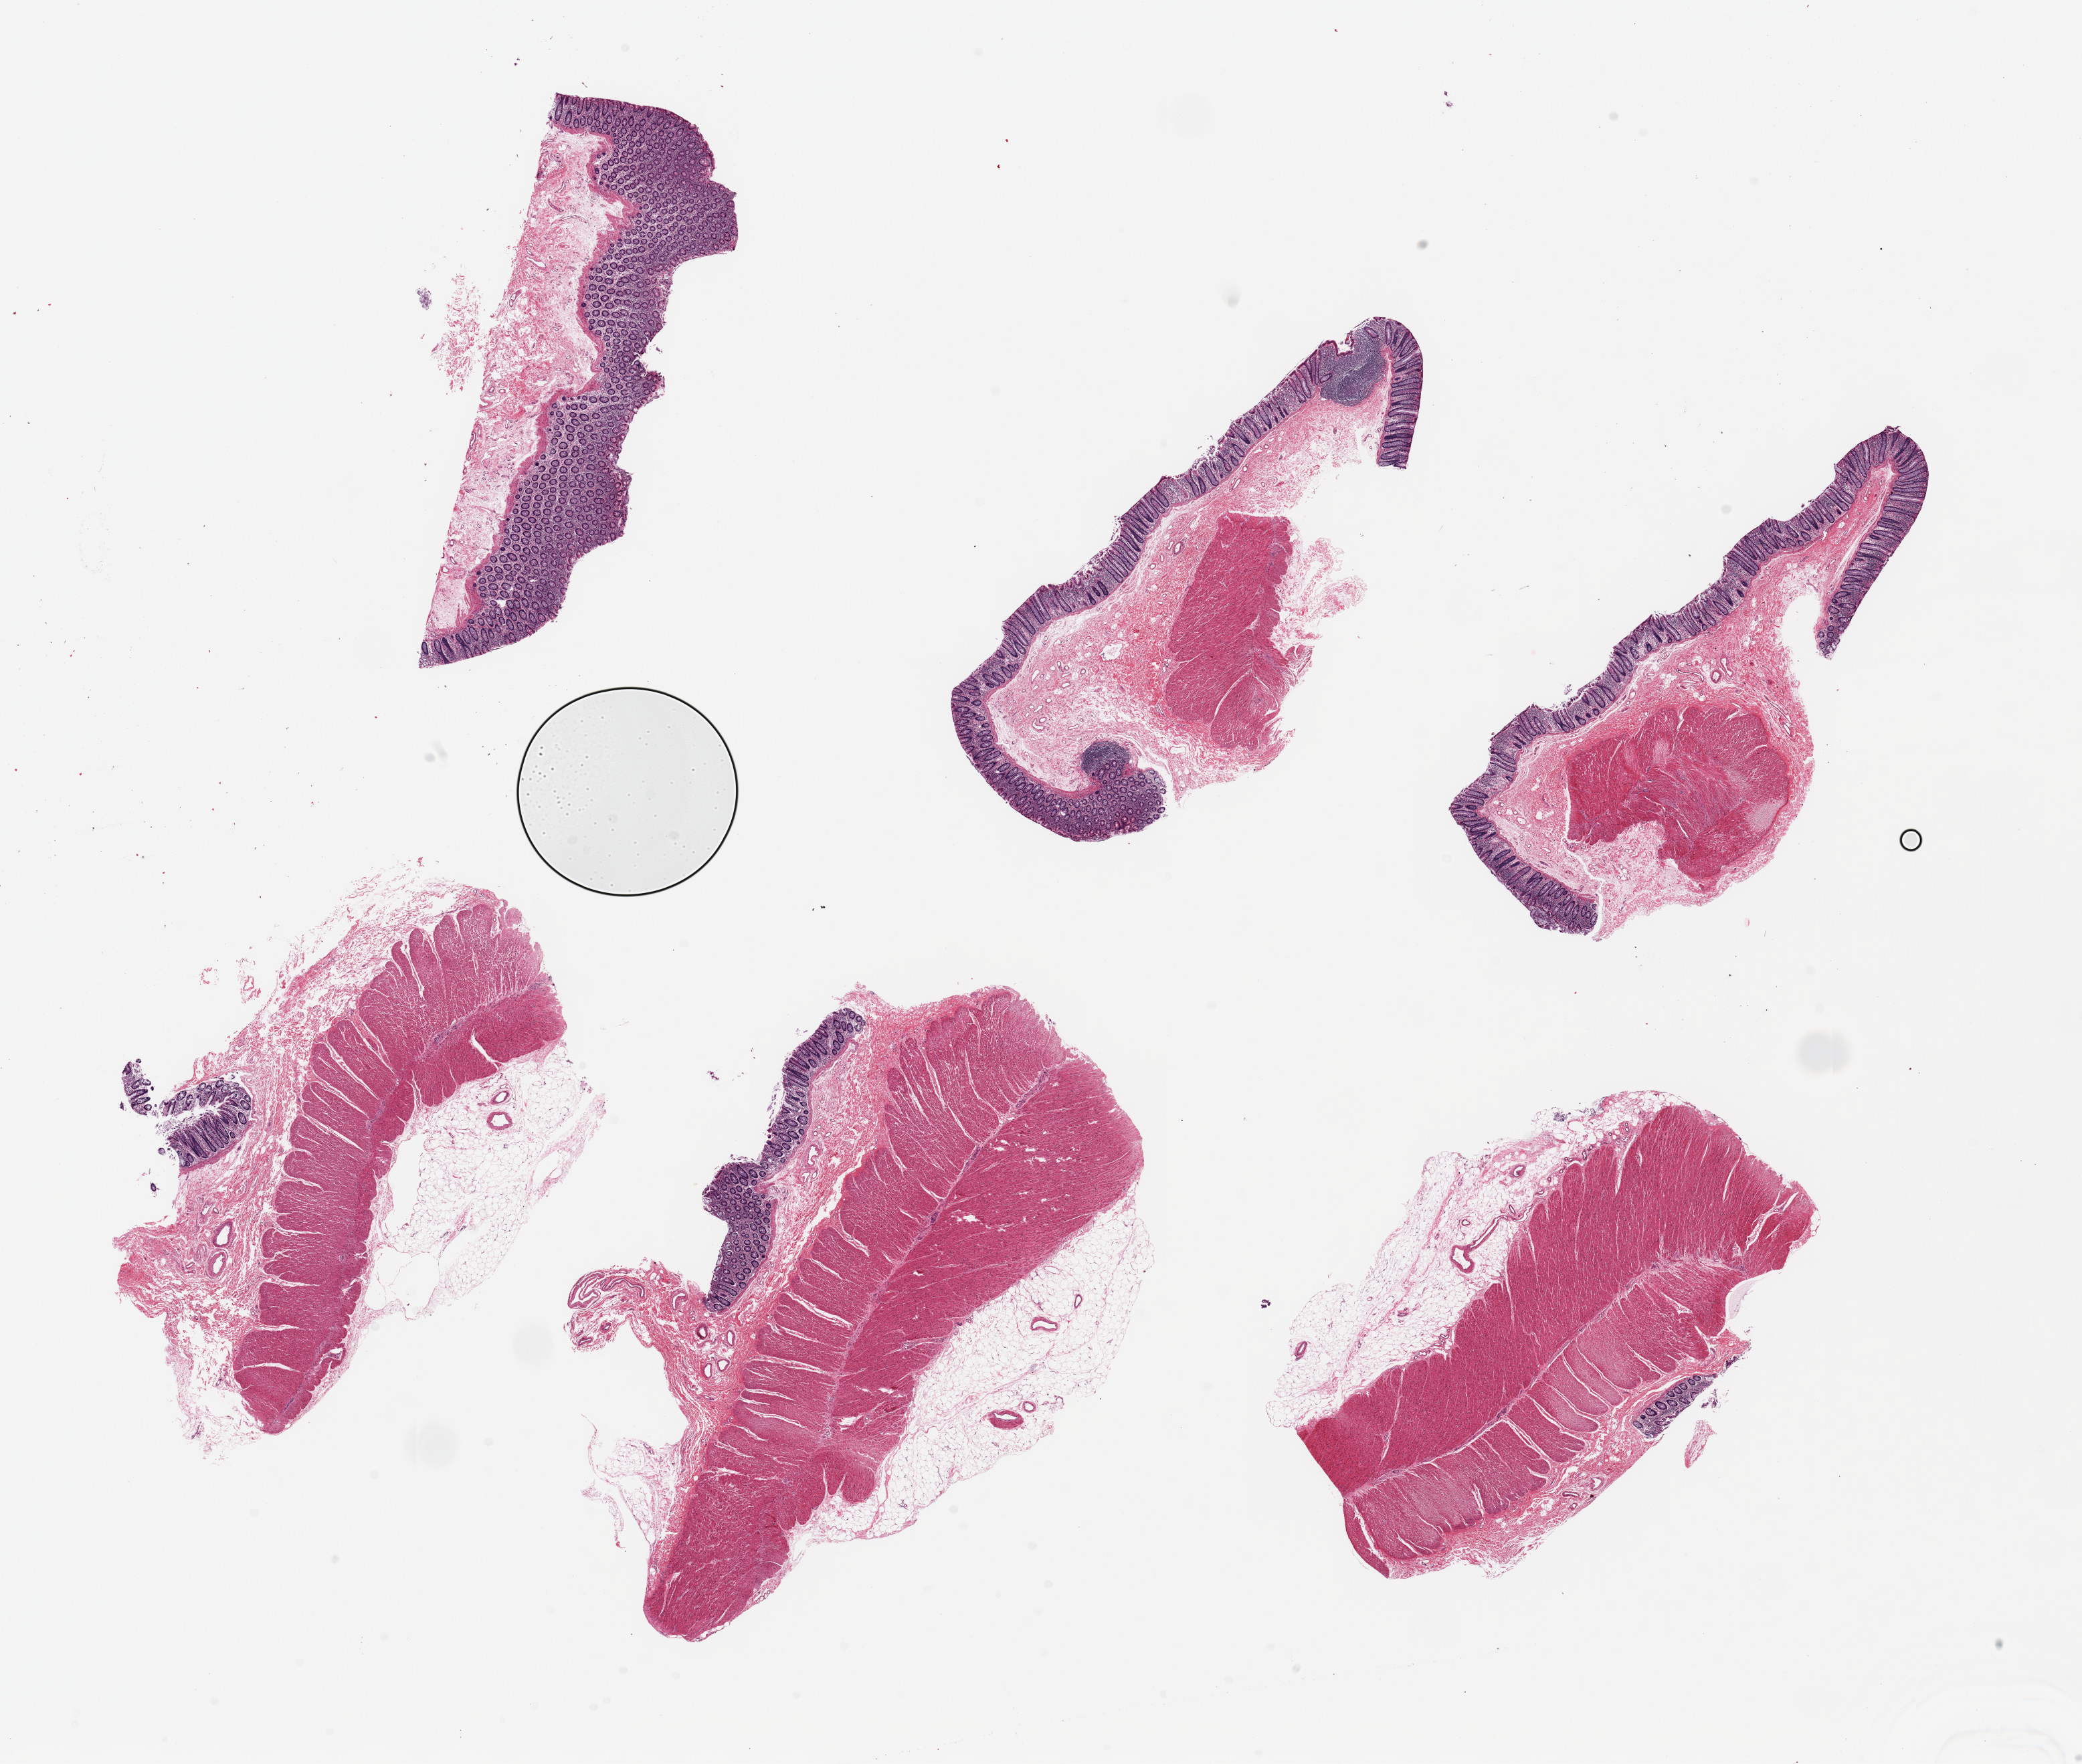
Hematoxylin and eosin (H&E) whole-slide image, brightfield, a low-resolution overview of the entire scanned area, about 24.6 x 20.9 mm (slide scanned at 20x); PAXgene-fixed paraffin-embedded (PFPE) section; sampled site (target tissue): transverse colon; donor tissue sample. Donor: male.
* pathologist's review note for this sample: 6 pieces ~~7x2mm, mucosa well preserved, ~10-20 thickness